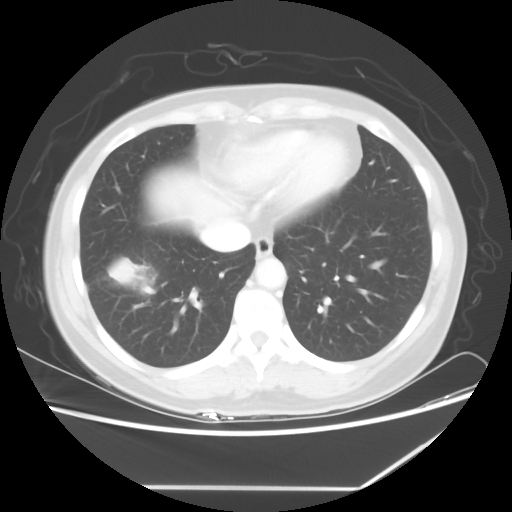
Chest CT, one axial slice; slice 20 of 60 in the series (ordered by position); reconstruction kernel STANDARD; 100 kVp; lung window (W 1500 / L -600 HU); 5 mm slice thickness; 512 × 512 image matrix, field of view 374 × 374 mm. Patient: female, 42 years. Case-level facts recorded for this patient, not image findings: clinical TNM (as recorded): T2 N1 M0.
Annotated regions visible in this slice (rectangle marked by the reading radiologist):
- lung tumour (recorded histology: adenocarcinoma): bounding box [x1, y1, x2, y2] px = [107, 253, 143, 285]